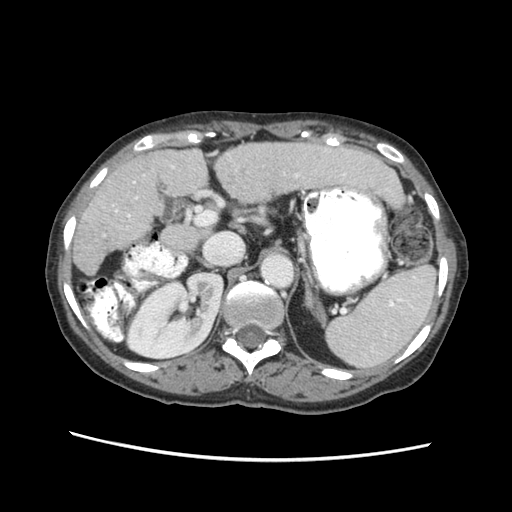
Contrast-enhanced abdominal CT (liver protocol), one axial slice; position 32 of 63 along the scan axis; reconstruction kernel STANDARD; soft-tissue window (W 400 / L 40 HU); 2.5 mm slice thickness; 512 × 512 image matrix. From the clinical record (not read from this slice): diagnosis: hepatocellular carcinoma (patient treated with transarterial chemoembolisation; whether this scan precedes or follows treatment is not stated here); TNM stage (as recorded): Stage-I; Child-Pugh class: B; tumour differentiation: well differentiated; tumour nodularity: uninodular.
Annotated regions visible in this slice (semi-automatically segmented with operator editing):
- abdominal aorta: bounding box <262,252,290,284> (left, top, right, bottom; pixels)
- liver parenchyma outside the tumour (the mass and vessels are separate outlines, so this box may not span the whole liver): <74,138,402,274>
- liver vessels: <102,162,343,235>